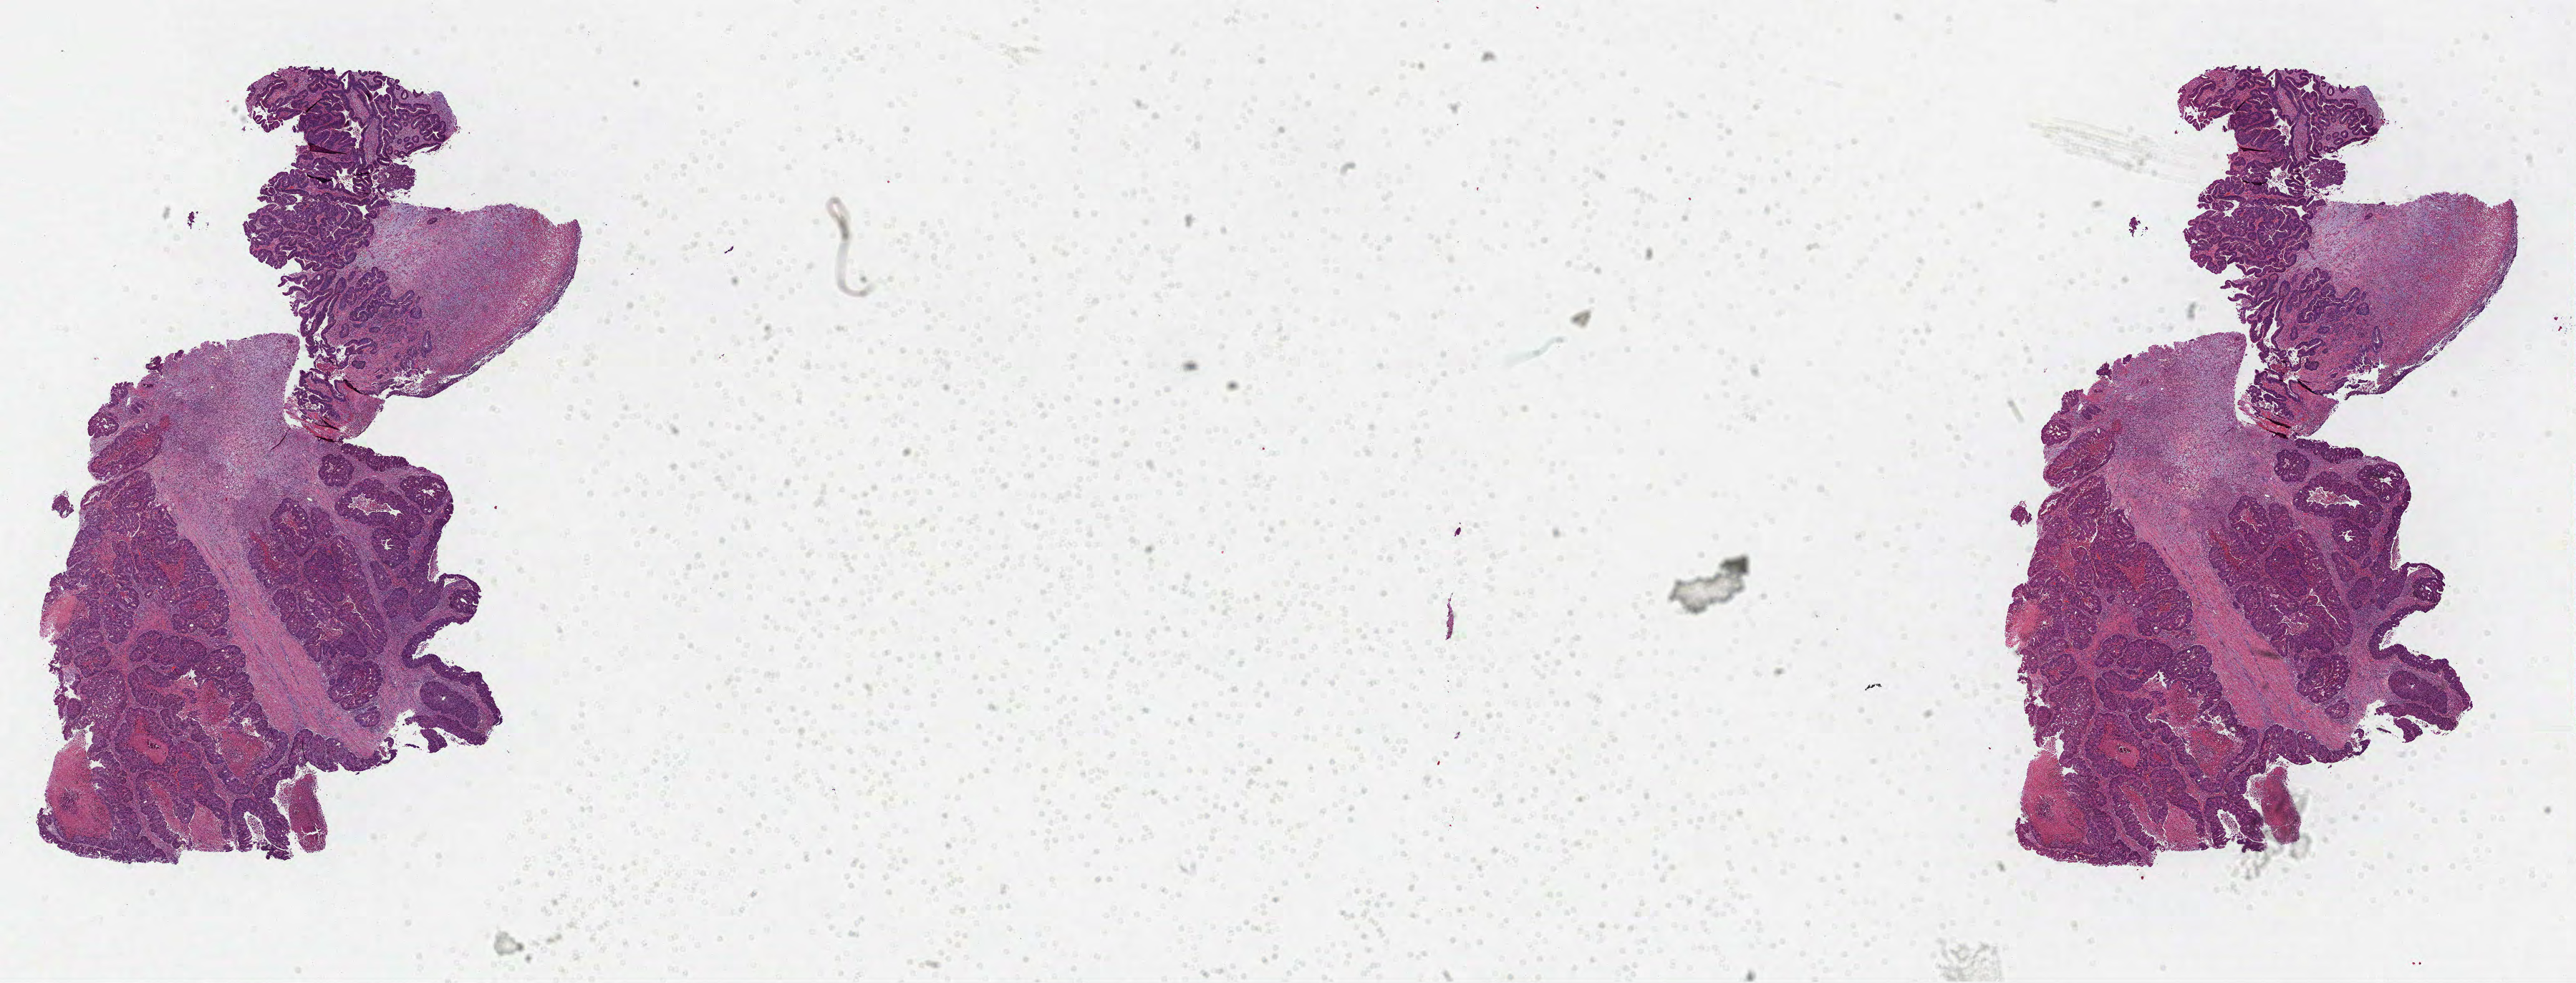
Whole-slide histology image, Hematoxylin and eosin (H&E) stained — whole scanned area (about 29.0 x 11.1 mm, acquisition: 40x scan) shown as a low-resolution overview; formalin-fixed paraffin-embedded (FFPE) diagnostic section; sample: primary tumour, colon. Patient: male, age at initial diagnosis 73 years.
Pathologic diagnosis: Adenocarcinoma, NOS (ascending colon). TNM: T3 N2b M0. AJCC pathologic stage: IIIC. Lymph nodes positive (case pathology): 11 of 23 examined.